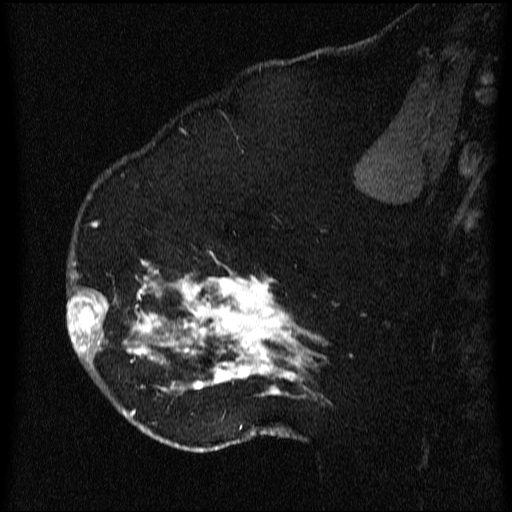
Breast MRI (dynamic contrast-enhanced), one sagittal slice. Position 42 of 64 along the scan axis. Dynamic contrast-enhanced series, image 2 of 3 at this slice position (ordered by acquisition). 1.5 T. TE 4.2 ms, TR 9.1 ms. 512 × 512 image matrix. Patient: female, 52 years.
Outlined on this slice (semi-automatic segmentation, software-assisted and operator-edited):
- analysis volume of interest (the breast-tissue region the enhancement analysis was run in; not a lesion): bounding box <68,203,333,438> (left, top, right, bottom; pixels)
- tumour enhancement mask (voxels above the 70 % enhancement threshold inside the analysis volume of interest): <68,225,325,437>